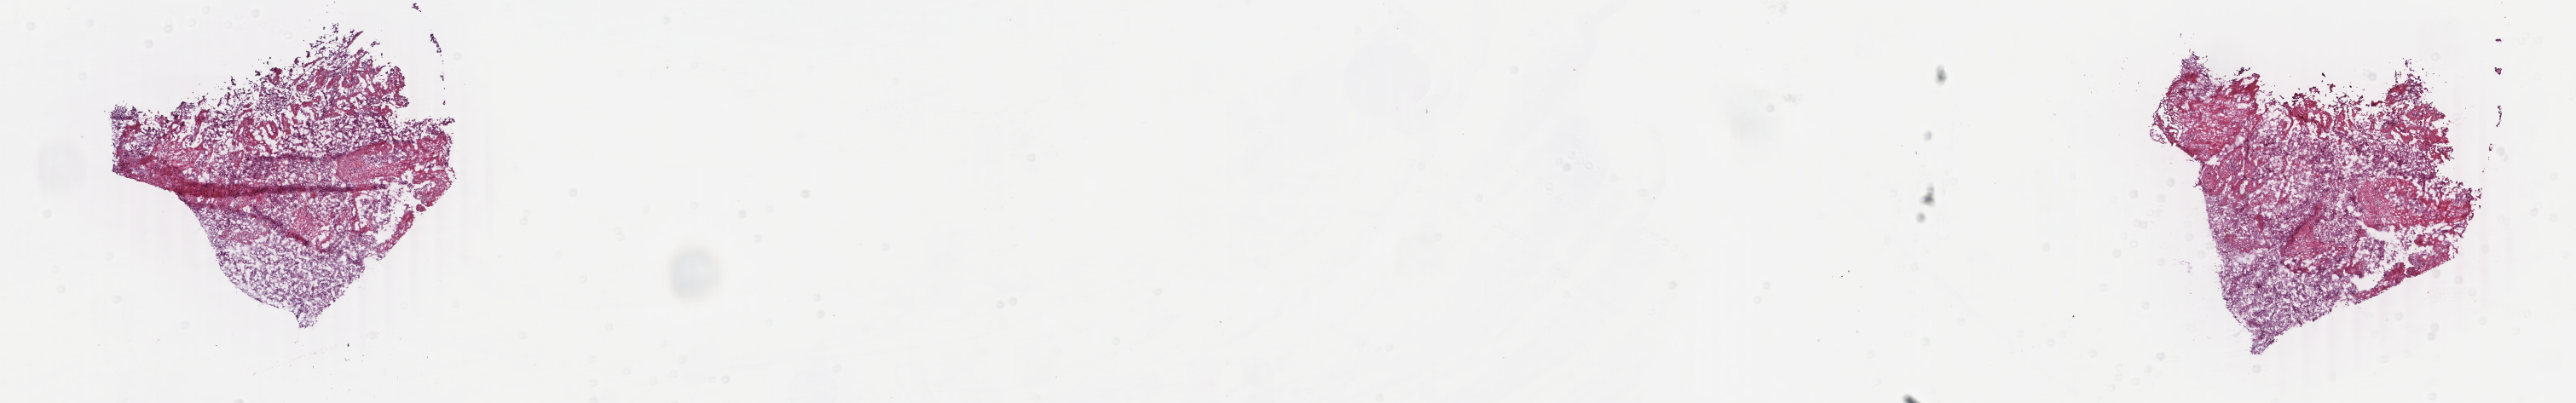
Digitized Hematoxylin and eosin (H&E) stained tissue section (whole slide), whole scanned area (about 24.0 x 3.8 mm, acquisition: 40x scan) shown as a low-resolution overview; frozen section from the bottom of the tissue portion; uterus, primary tumour sample. Female, age 72 years at initial diagnosis. Histologic grade: G3 (poorly differentiated). Pathologist review of this section (percent, as recorded): tumour cells 60%, tumour nuclei 72%, normal cells 36%, stromal cells 2%, necrosis 2%. Infiltration values recorded for this section: lymphocyte infiltration 5%, monocyte infiltration 0%, neutrophil infiltration 0%.
Lymph nodes positive (case pathology): 0 of 8 examined. Diagnosis: Endometrioid adenocarcinoma, NOS (endometrium). FIGO stage: IIA.